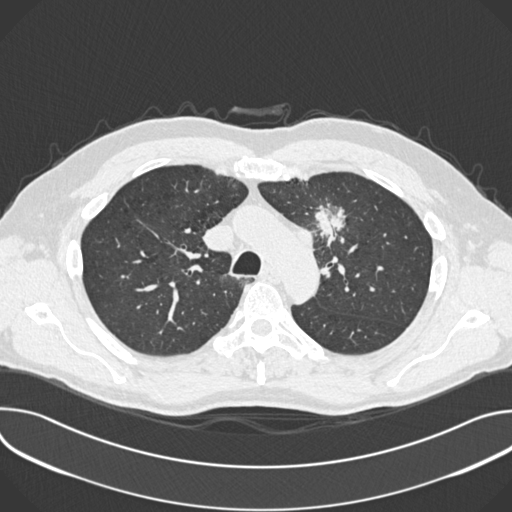
Low-dose screening chest CT, one axial slice. Slice 268 of 361 in the series (ordered by position). Lung window (W 1500 / L -600 HU). 1 mm slice thickness. 512 × 512 image matrix, field of view 380 × 380 mm.
Outlined on this slice (expert manual segmentation):
- lesion 1 (tumor, upper lobe of left lung): bounding box [x1, y1, x2, y2] px = [315, 208, 345, 244]